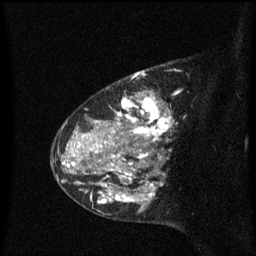
Breast MRI (dynamic contrast-enhanced), one sagittal slice. Slice 43 of 60 in the series (ordered by position). Dynamic contrast-enhanced series, image 2 of 3 at this slice position (ordered by acquisition). 1.5 T. TE 4.2 ms, TR 8.4 ms. 2 mm slice thickness. 256 × 256 image matrix. Patient: female, 48 years. Case-level facts recorded for this patient, not image findings: setting: breast cancer imaged before/during neoadjuvant chemotherapy; receptor status: HR-positive, HER2-negative.
Annotated regions visible in this slice (semi-automatically segmented with operator editing):
- analysis volume of interest (the breast-tissue region the enhancement analysis was run in; not a lesion): bounding box <80,78,175,217> (left, top, right, bottom; pixels)
- tumour enhancement mask (voxels above the 70 % enhancement threshold inside the analysis volume of interest): <84,78,173,206>